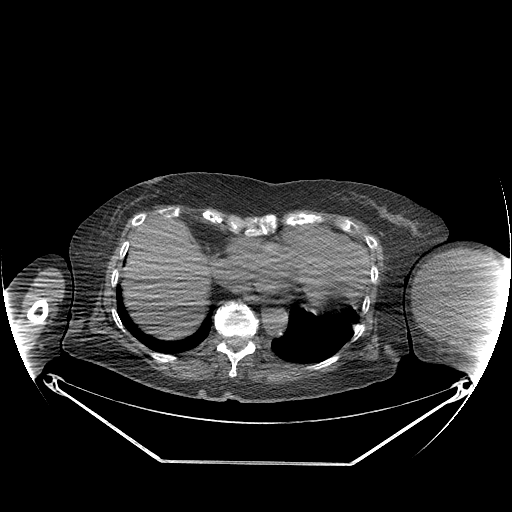
CT of an extremity soft-tissue mass (from a PET/CT study), one axial slice. Position 149 of 267 along the scan axis. Reconstruction kernel STANDARD. Soft-tissue window (W 400 / L 40 HU). 3.75 mm slice thickness. 512 × 512 image matrix, field of view 500 × 500 mm. Female patient. Case-level facts recorded for this patient, not image findings: histological type: pleiomorphic leiomyosarcoma; grade: high; site of the primary tumour: left biceps.
Structures marked on this image (expert contour drawn on MRI and transferred to this co-registered scan by the dataset authors):
- gross tumour volume including surrounding oedema: bounding box [x1, y1, x2, y2] px = [416, 249, 497, 325]
- gross tumour volume (mass): [416, 249, 497, 325]